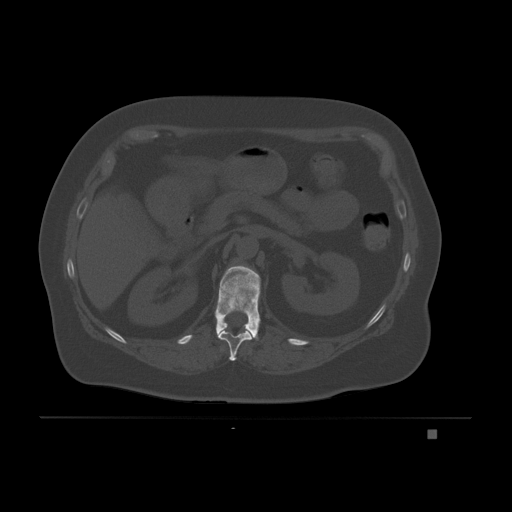
CT including the spine, one axial slice. Slice 83 of 221 in the series (ordered by position). Bone window (W 1800 / L 400 HU). 3 mm slice thickness. 512 × 512 image matrix, field of view 474 × 474 mm. Female patient, age 63 years. From the clinical record (not read from this slice): primary cancer: breast.
Annotated regions visible in this slice (semi-automatically segmented with operator editing):
- T11 vertebra: bounding box (x1, y1, x2, y2) in pixels: (217, 330, 252, 361)
- T12 vertebra: (215, 266, 261, 340)